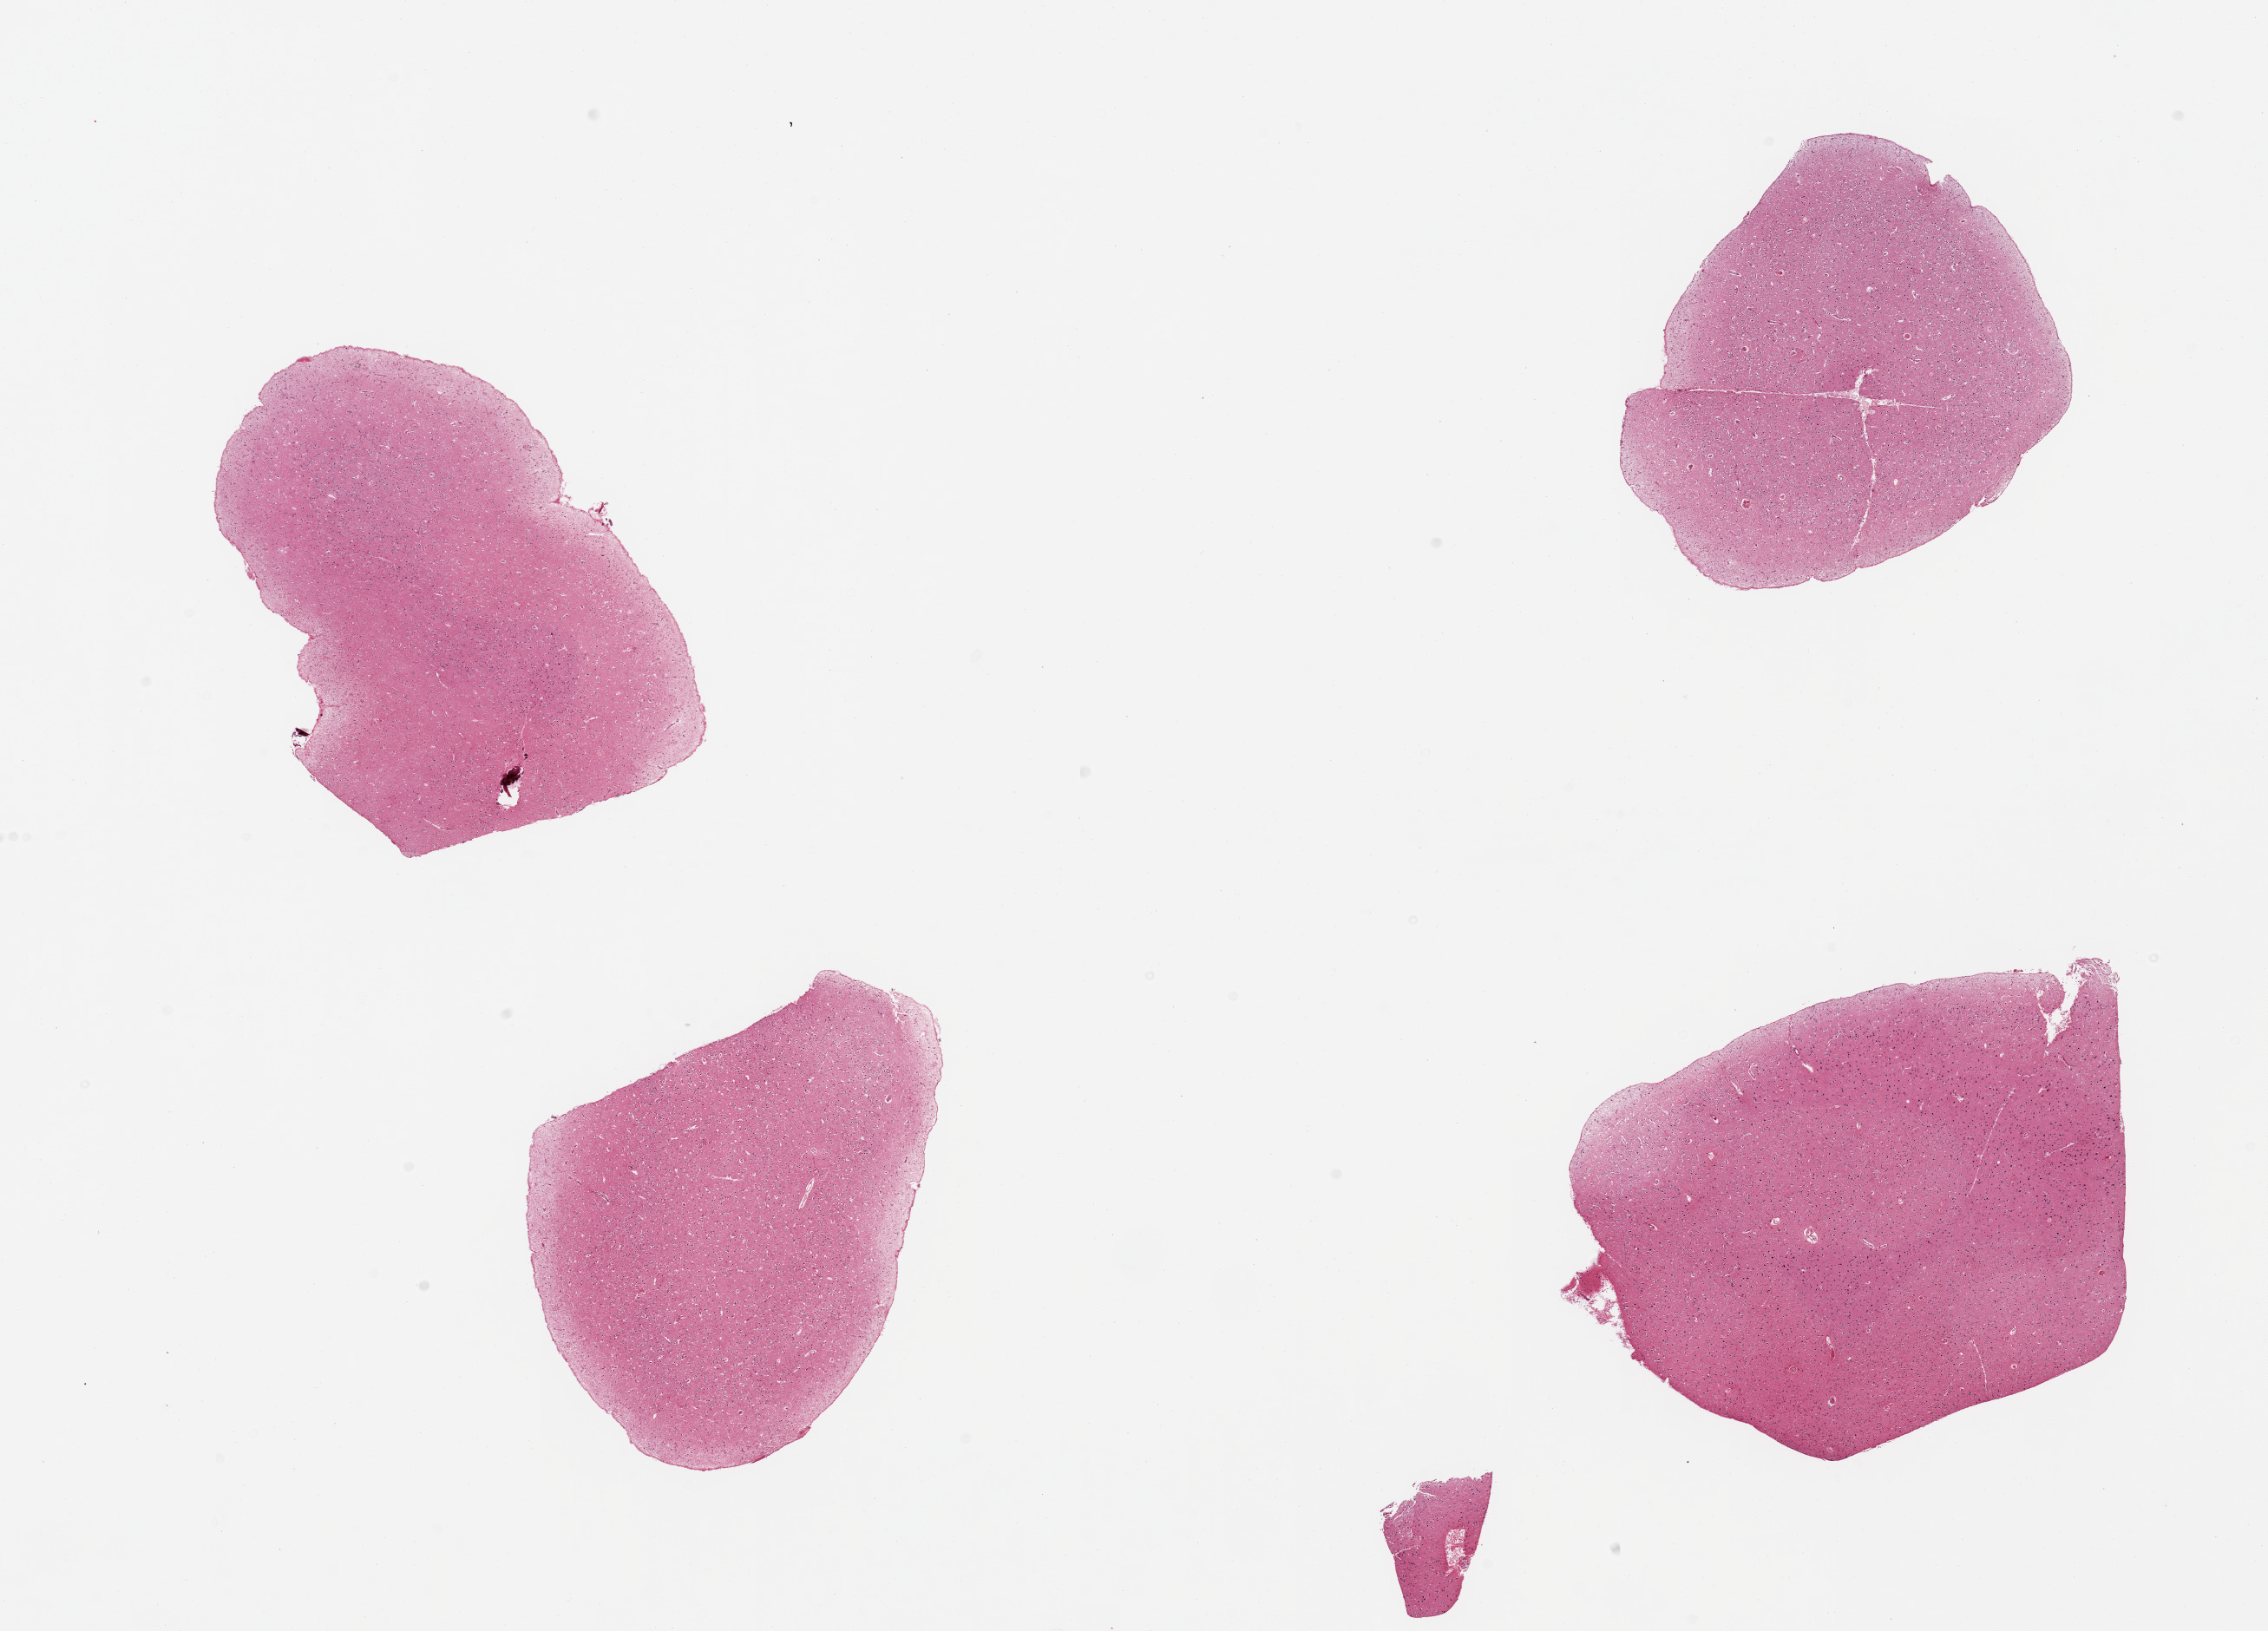
Digitized H&E-stained section, brightfield — low-resolution overview of the scanned area, about 20.7 x 14.9 mm (from a 20x scan), PAXgene-fixed paraffin-embedded (PFPE) section, target tissue: cerebral cortex, tissue donor sample. Donor sex: male.
Reviewer comment on this tissue sample: 4 pieces.